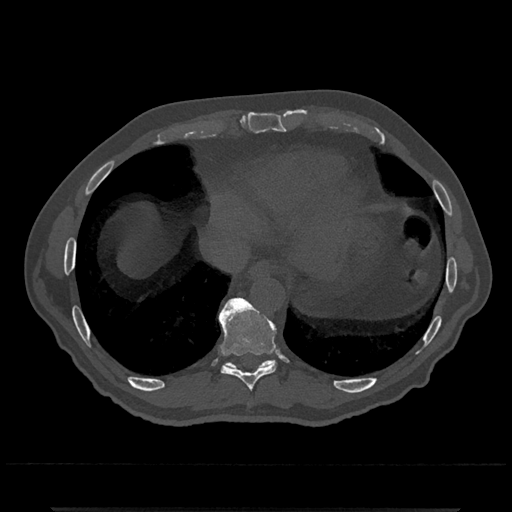
CT including the spine, one axial slice. Position 598 of 797 along the scan axis. Reconstruction kernel Br40s/3. Bone window (W 1800 / L 400 HU). 0.5 mm slice thickness. 512 × 512 image matrix. Patient: male, 67 years. Case-level facts recorded for this patient, not image findings: primary cancer: prostate.
Annotated regions visible in this slice (semi-automatic segmentation, software-assisted and operator-edited):
- T10 vertebra: bounding box (x1, y1, x2, y2) in pixels: (224, 298, 276, 368)
- T9 vertebra: (218, 297, 277, 391)